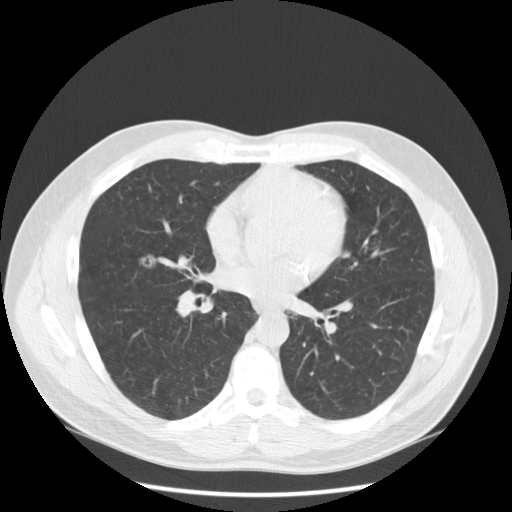
Low-dose screening chest CT, one axial slice; position 106 of 234 along the scan axis; reconstruction kernel STANDARD; lung window (W 1500 / L -600 HU); 2.5 mm slice thickness; 512 × 512 image matrix, field of view 385 × 385 mm.
Annotated regions visible in this slice (manually delineated by an expert):
- lesion 1 (tumor, middle lobe of right lung): bounding box (x1, y1, x2, y2) in pixels: (138, 254, 156, 268)